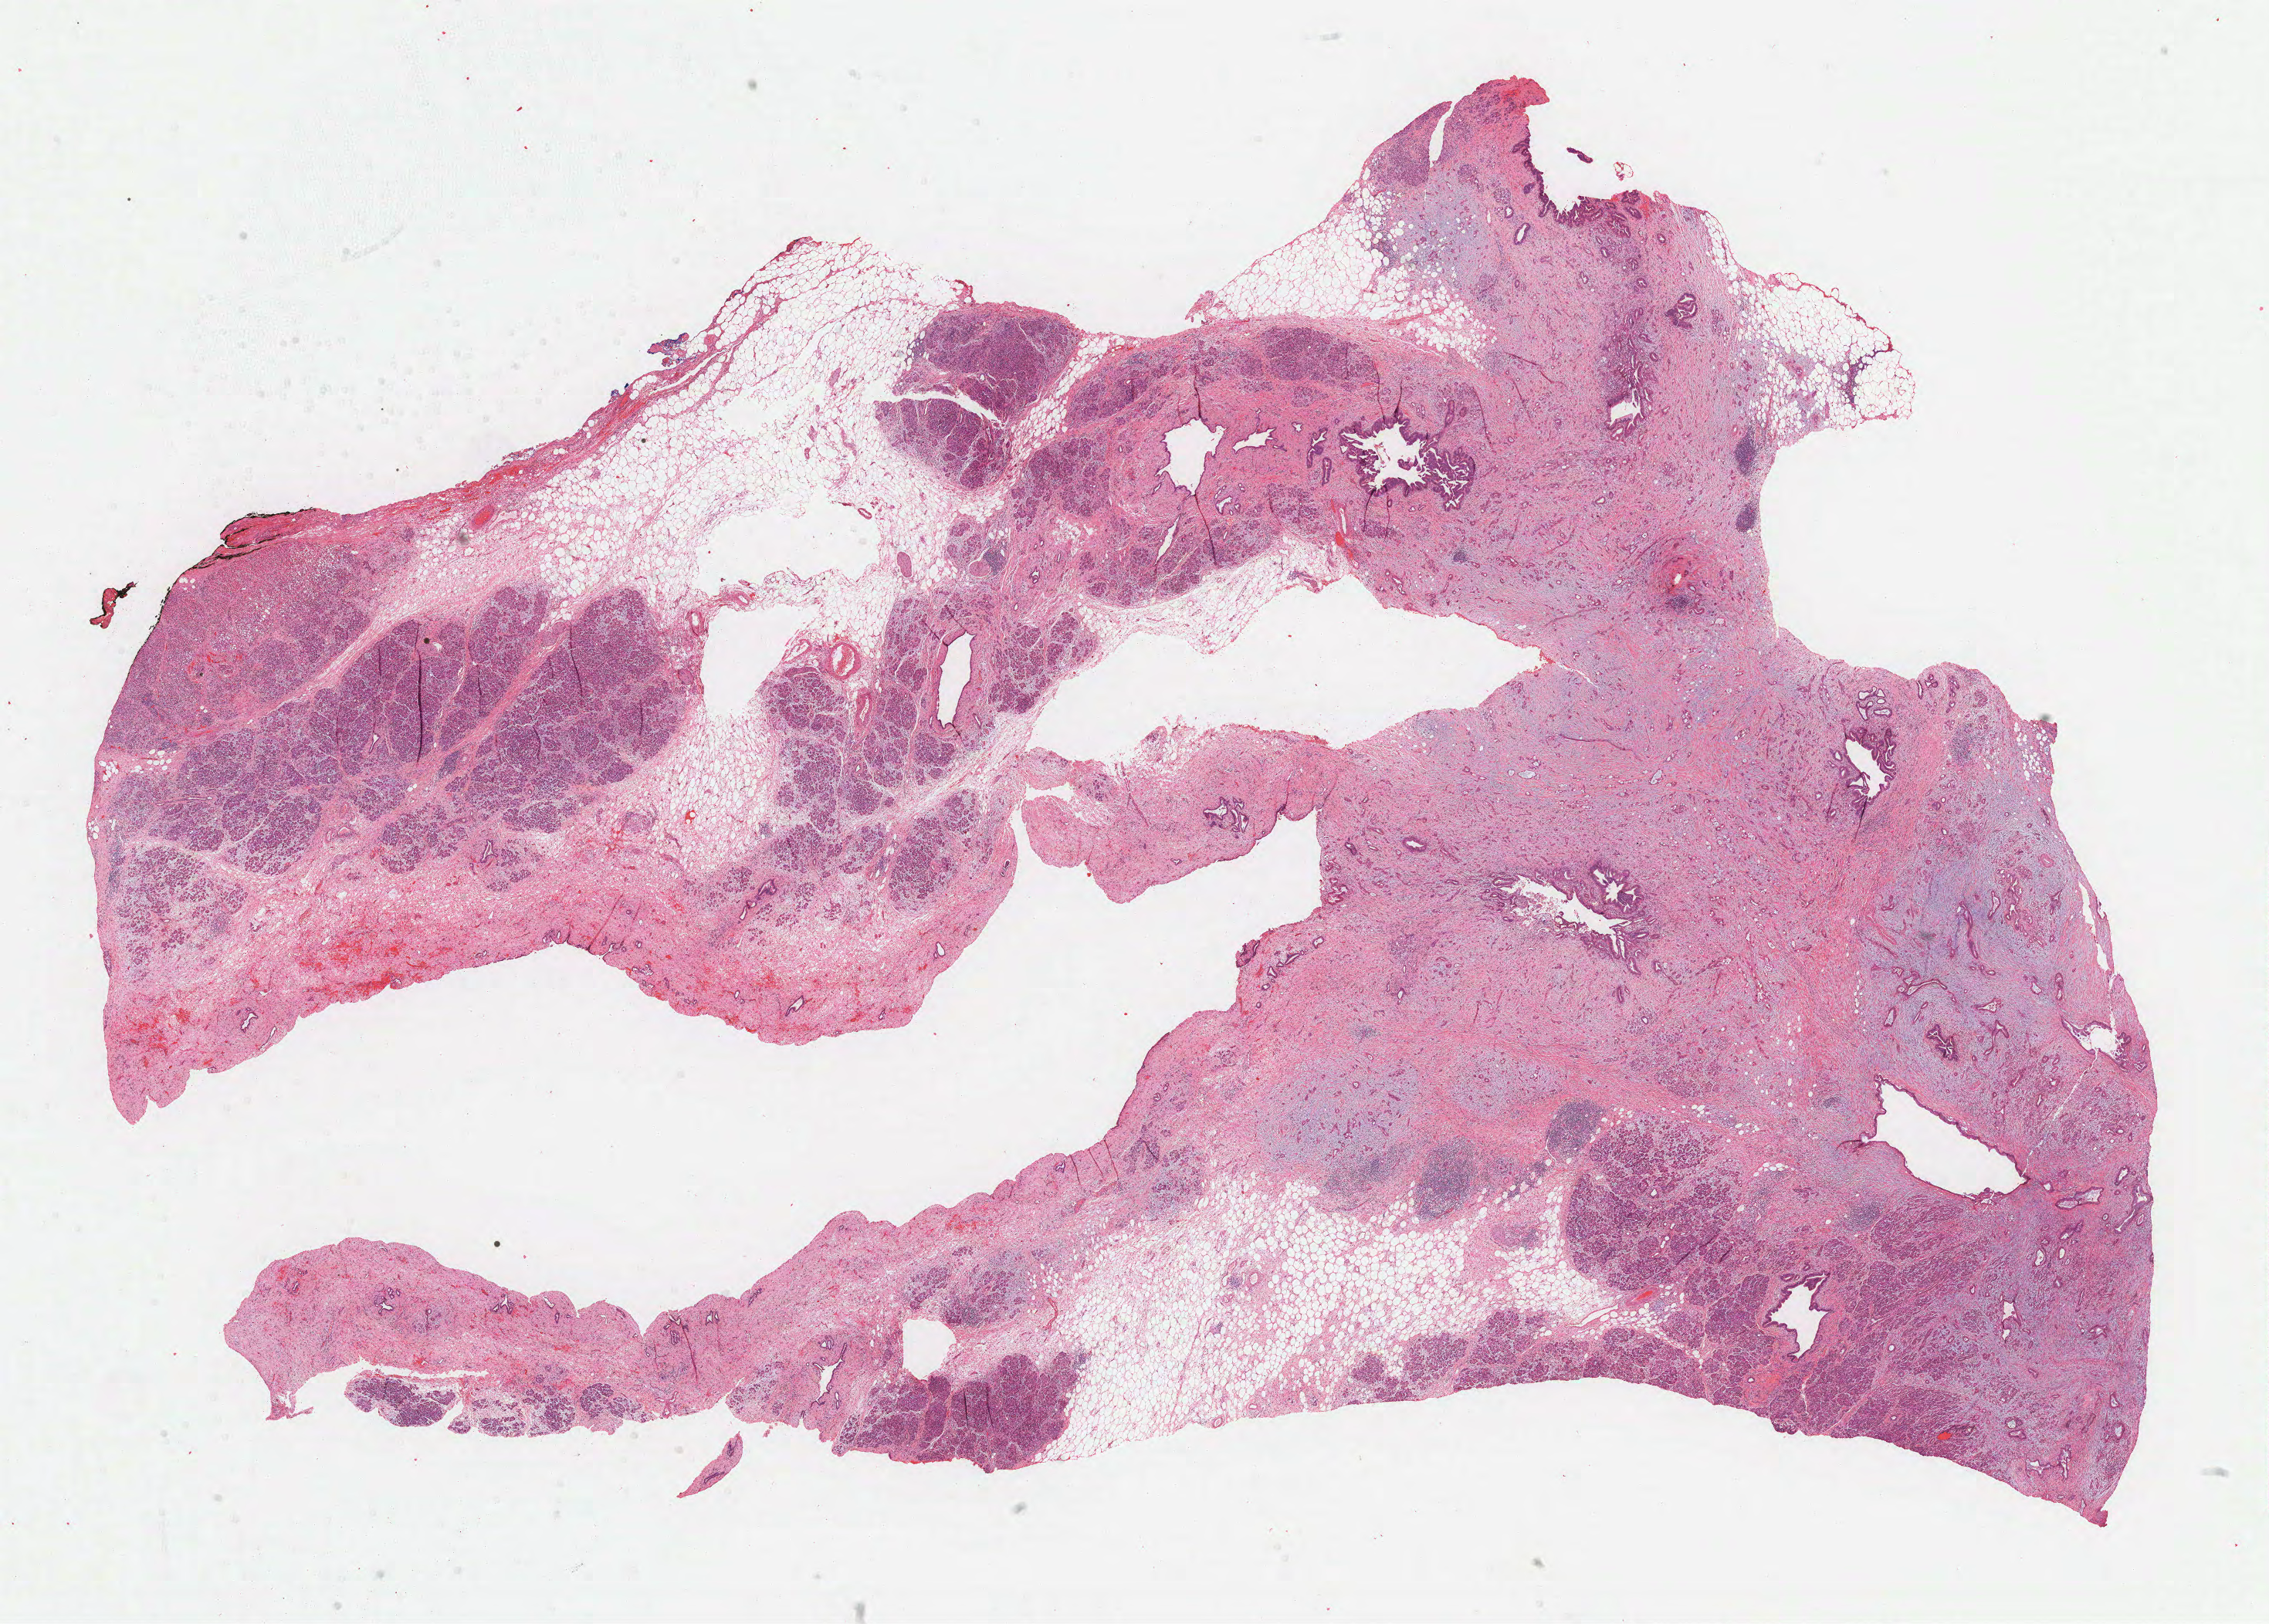
H&E-stained whole-slide image, a low-resolution overview of the entire scanned area, about 23.7 x 17.0 mm (acquisition: 40x scan). Formalin-fixed paraffin-embedded (FFPE) diagnostic section. Primary tumour sample from the pancreas. Male, age 40 years at initial diagnosis. Histologic grade: G2 (moderately differentiated).
• lymph nodes positive (case pathology): 0 of 35 examined
• pathologic diagnosis: Infiltrating duct carcinoma, NOS (head of pancreas)
• AJCC pathologic stage: IA (7th edition)
• TNM: T1 N0 MX